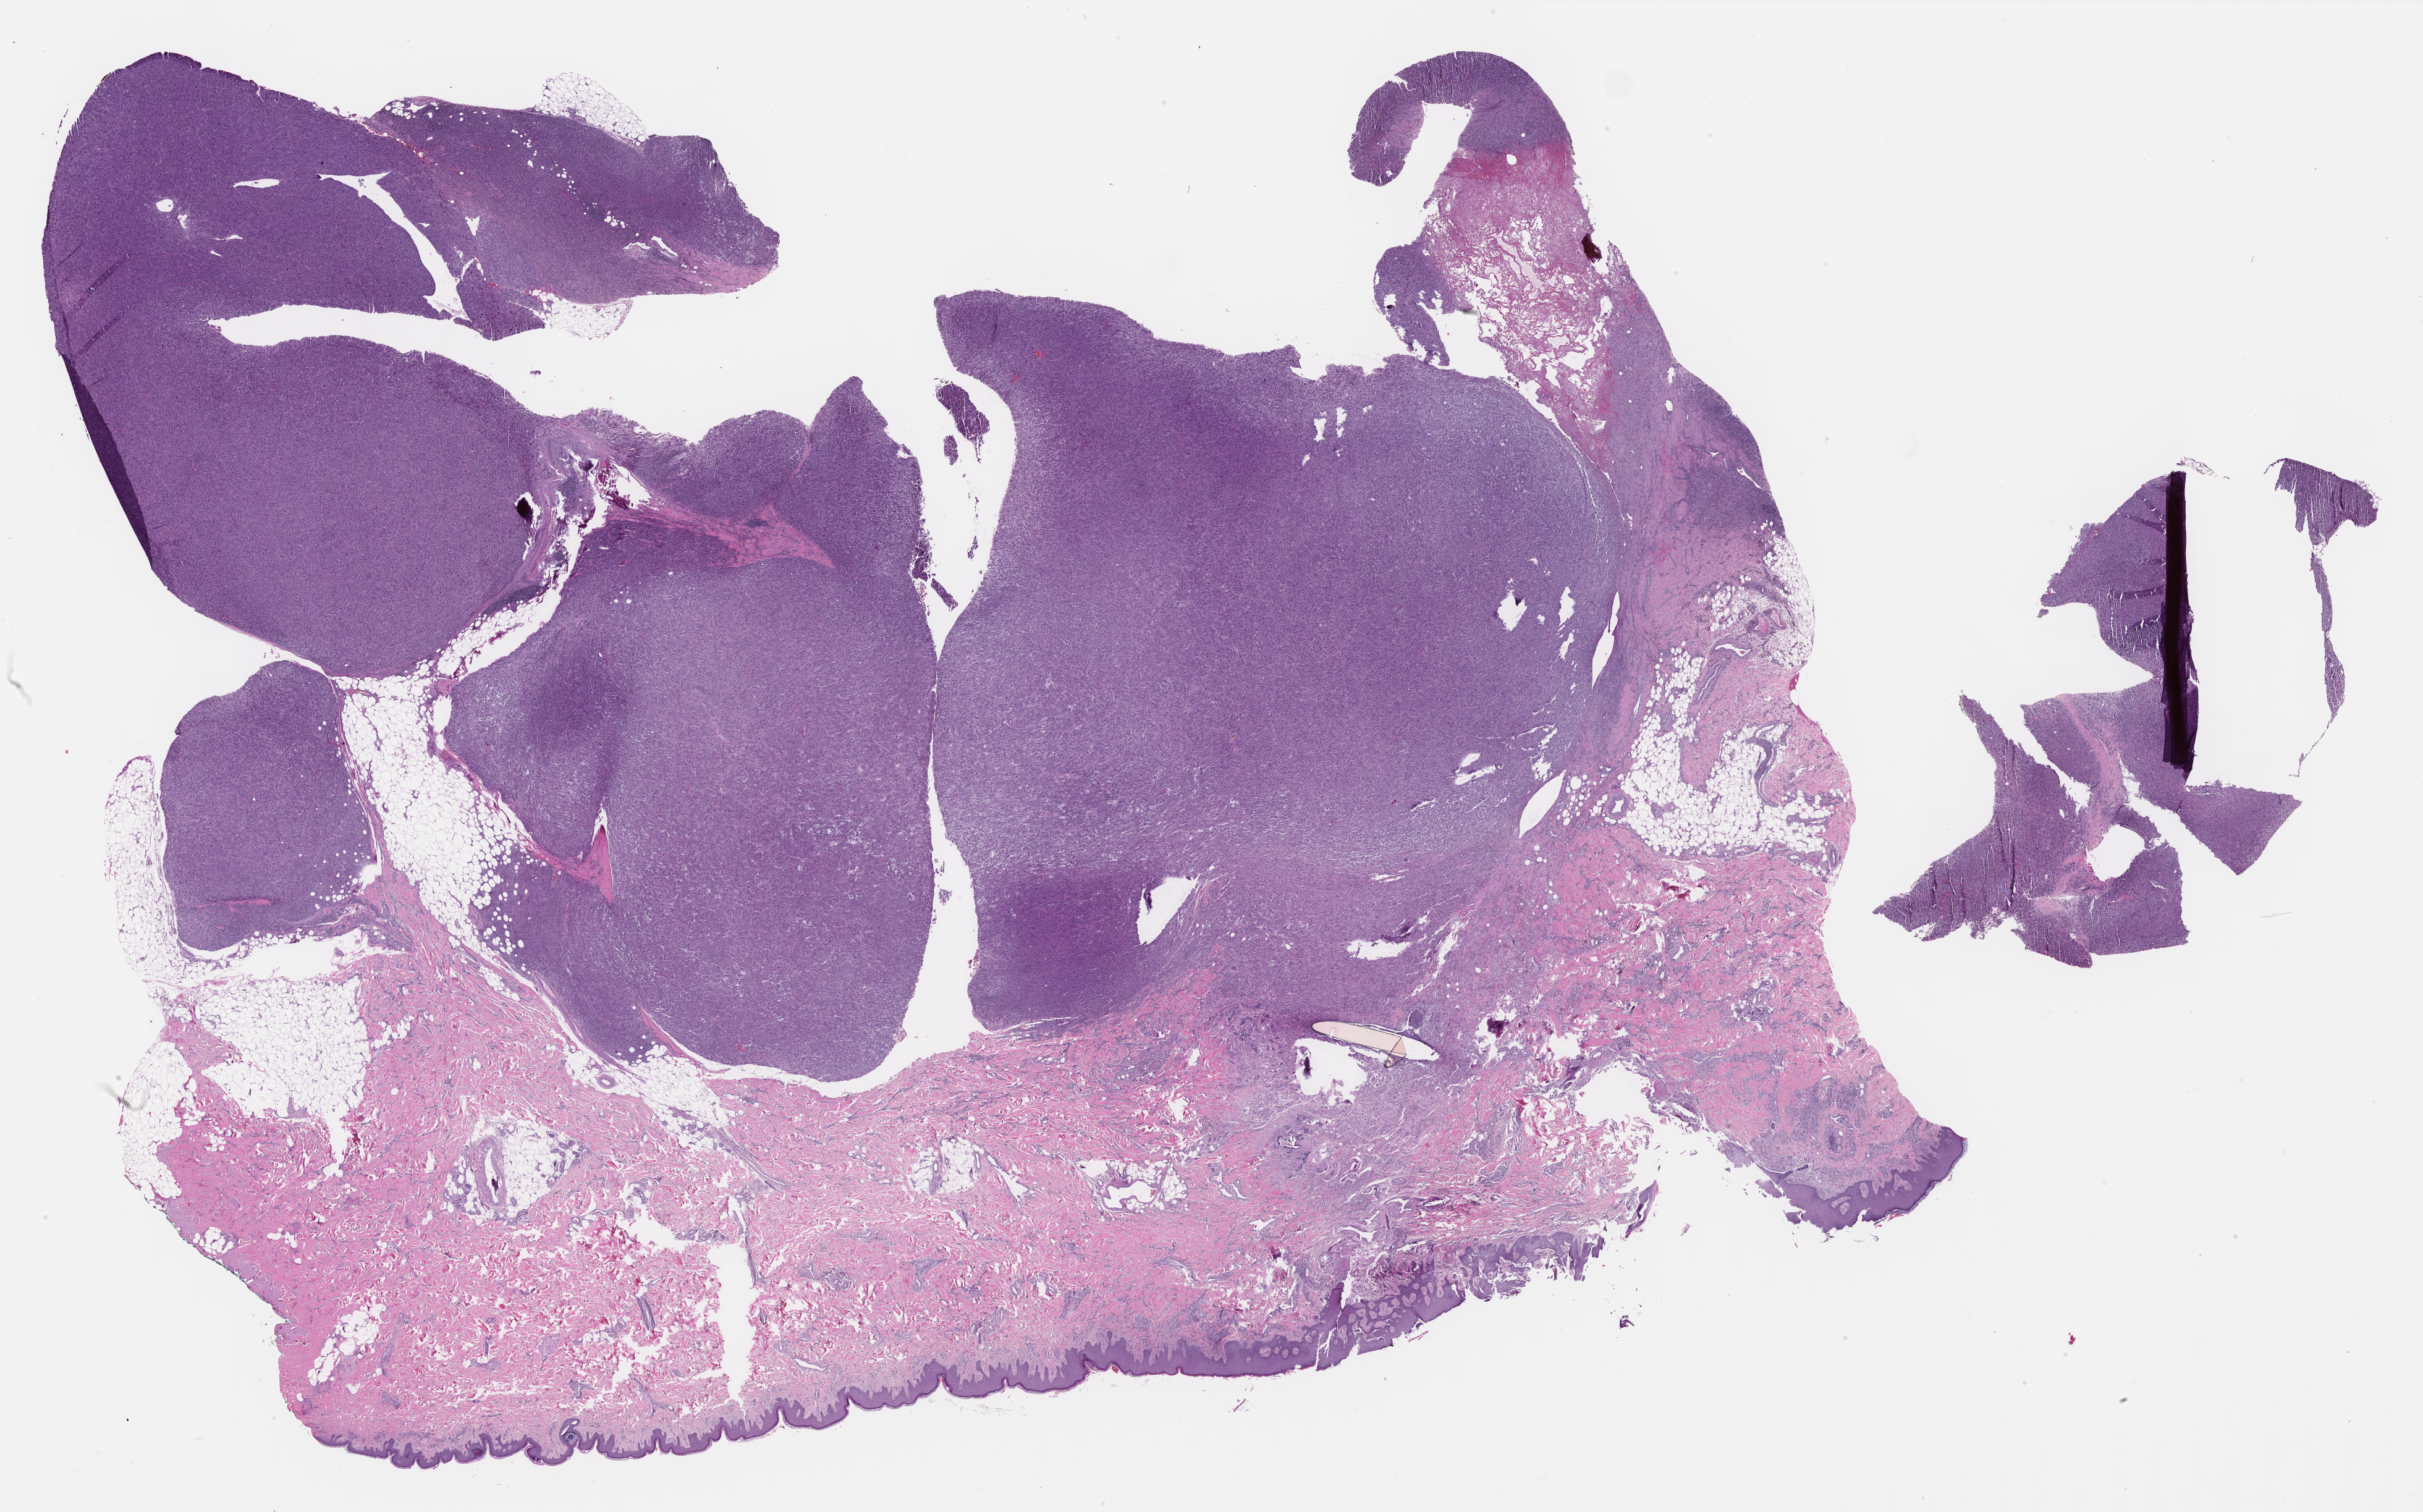
Whole-slide histology image, H&E — a low-resolution overview of the entire scanned area, about 31.5 x 19.7 mm. FFPE section. Primary tumour sample from the connective, subcutaneous and other soft tissues. Male, age 63 years at initial diagnosis.
Histologic diagnosis: Malignant fibrous histiocytoma (connective, subcutaneous and other soft tissues of lower limb and hip).